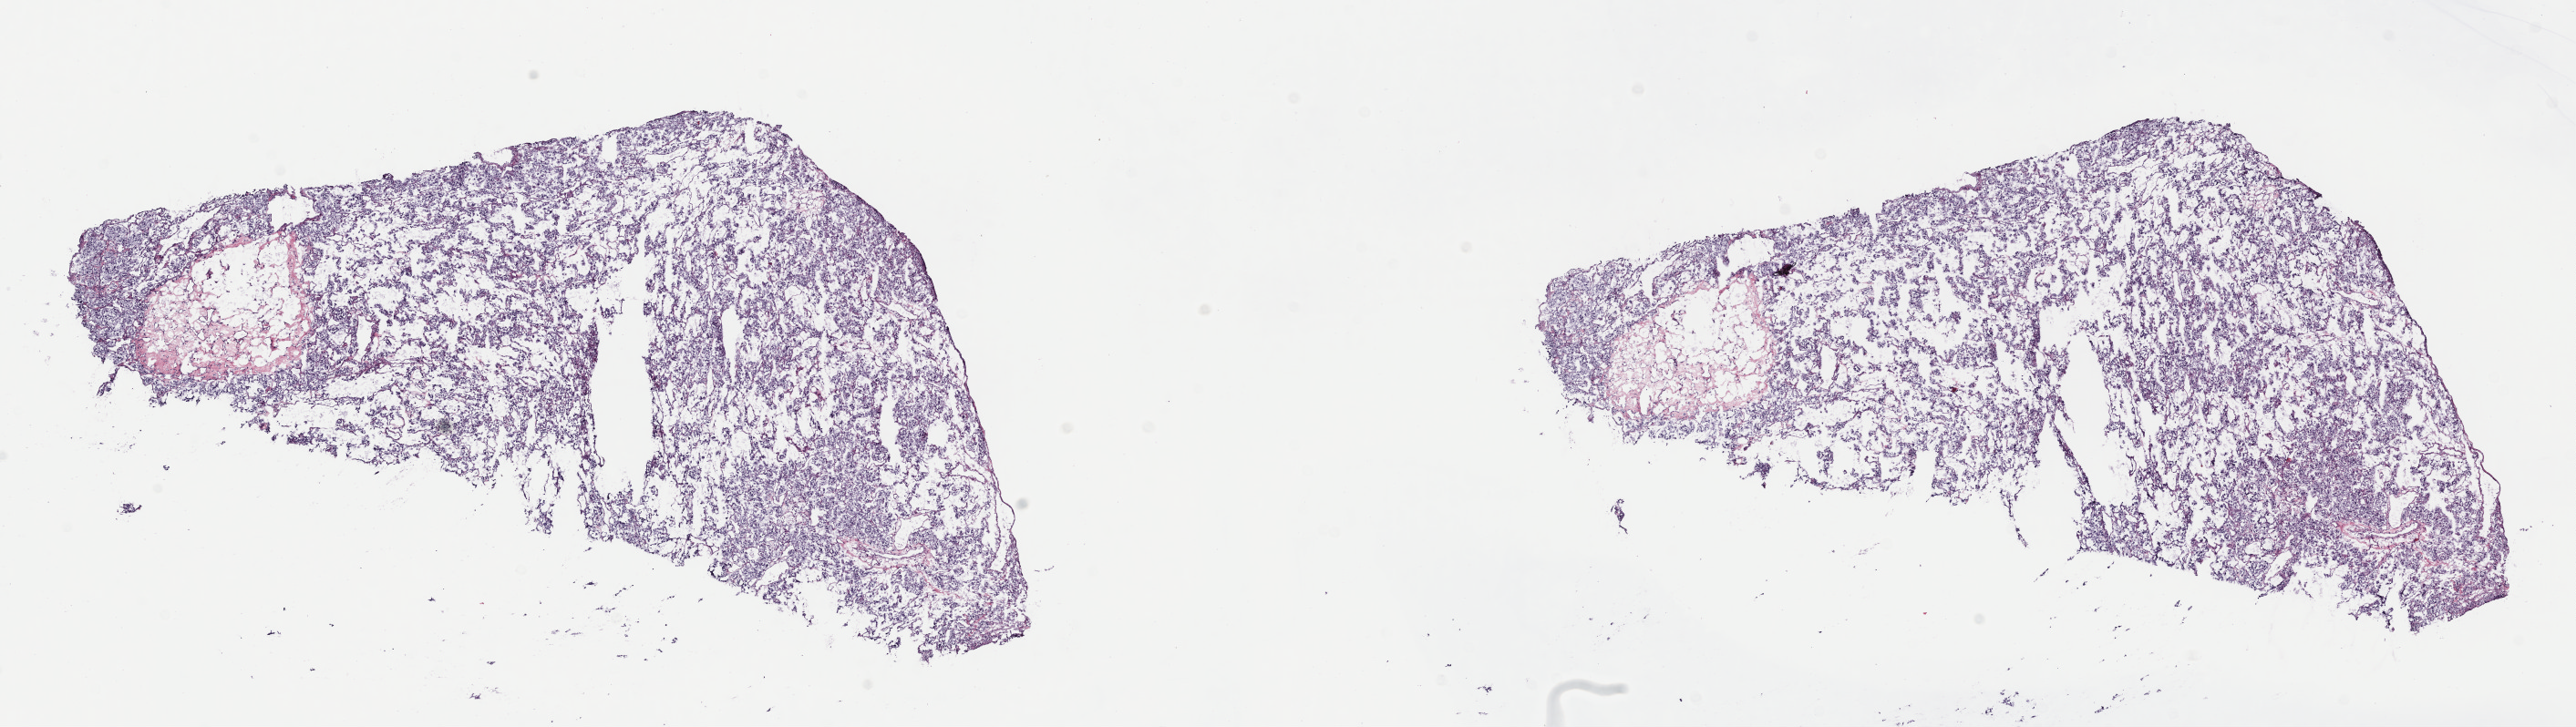
H&E-stained whole-slide image — a low-resolution overview of the entire scanned area, about 22.3 x 6.3 mm (slide scanned at 40x), frozen section from the top of the tissue portion, sample: primary tumour, adrenal gland. Male patient; age at initial diagnosis 27 years.
Diagnosis: Pheochromocytoma, malignant.